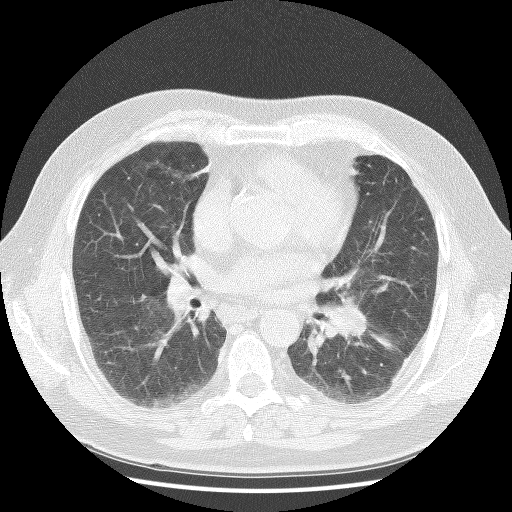
Low-dose screening chest CT, axial slice. Baseline annual screen. Lung window (W 1500 / L -600 HU). 120 kVp. Male, age 59 years at enrolment. Current smoker at enrolment.
Expert-annotated lung lesion, bounding box <304,287,379,360> (left, top, right, bottom; pixels). The exam's reader record, not a measurement of the box and not confirmed to be the same lesion: non-calcified nodule or mass ≥4 mm, right upper lobe, 4 × 4 mm, soft tissue attenuation. Note: the box lies in the patient's left hemithorax on this image, whereas the reader's record names the right lung; they may be different findings. Official screen result: positive, change unspecified: nodule(s) >= 4 mm or enlarging nodule(s), mass(es), or other non-specific abnormalities suspicious for lung cancer. Participant outcome: lung cancer diagnosed 20 days after this screen — non-small cell carcinoma, left hilum, stage IV (AJCC 6th edition).